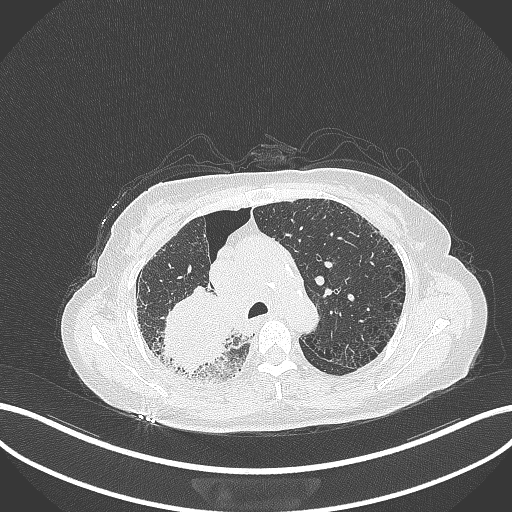
Chest CT, one axial slice; position 239 of 408 along the scan axis; reconstruction kernel B70f; 120 kVp; lung window (W 1500 / L -600 HU); 1 mm slice thickness; 512 × 512 image matrix, field of view 400 × 400 mm. Patient: female, 64 years. Case-level facts recorded for this patient, not image findings: clinical TNM (as recorded): T3 N3 M0.
Annotated regions visible in this slice (rectangle marked by the reading radiologist):
- lung tumour (recorded histology: squamous cell carcinoma): box from (x=160, y=280) to (x=233, y=371) px